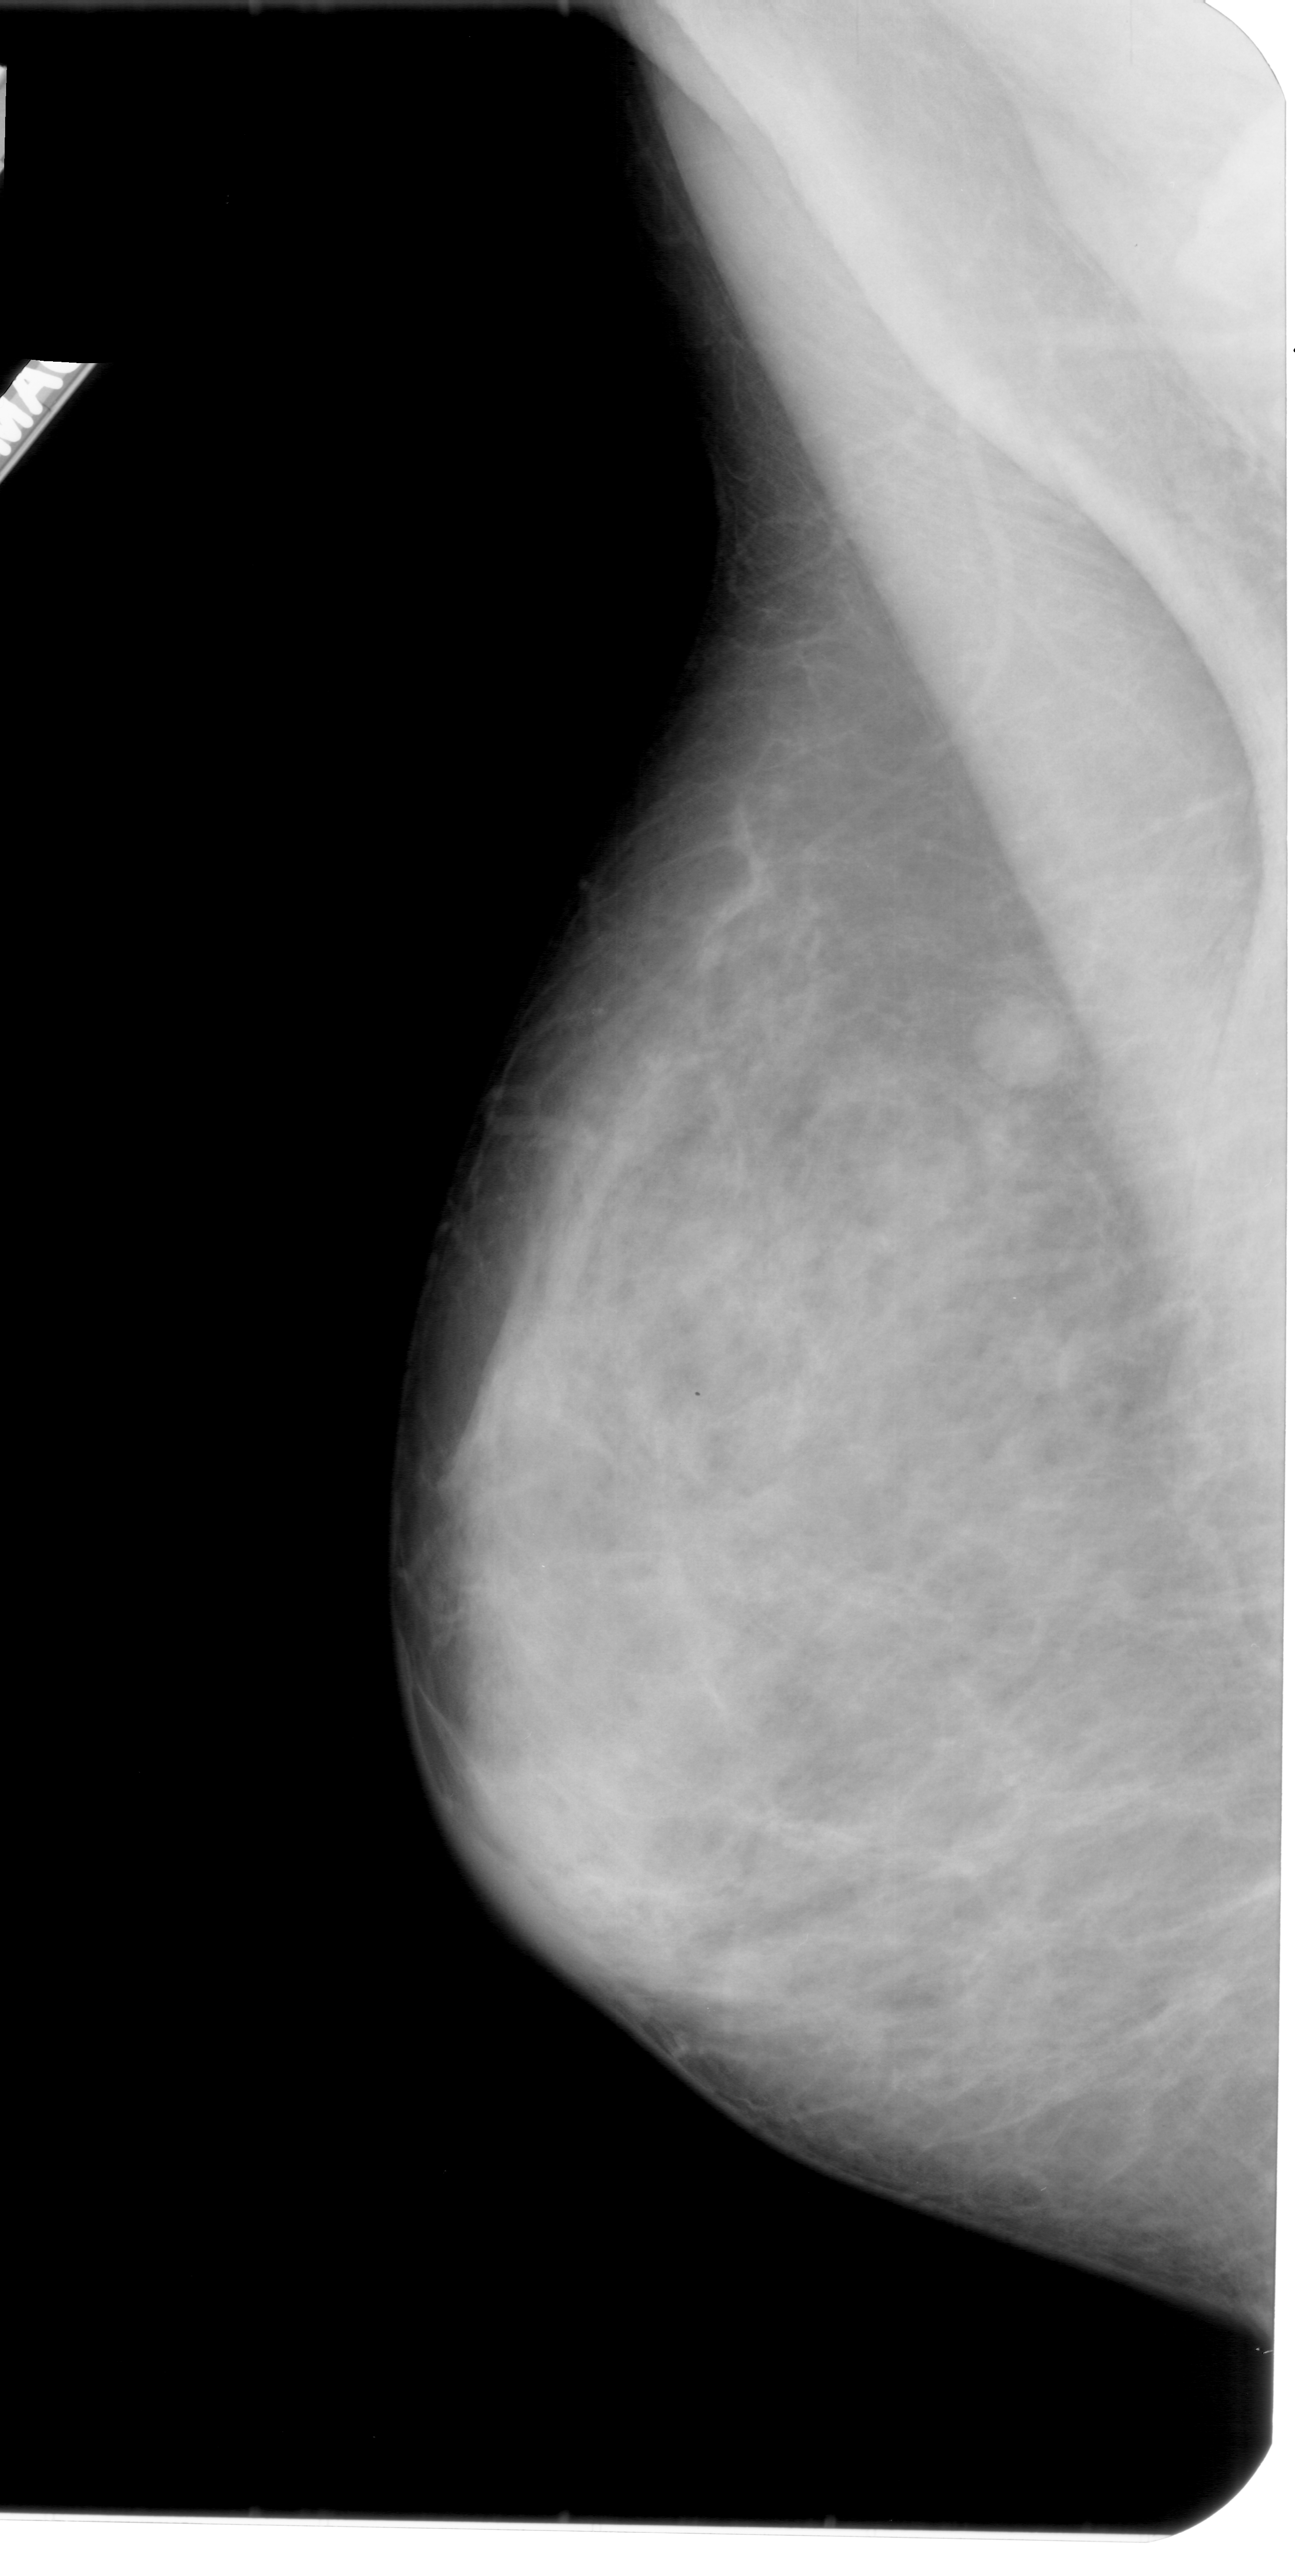
Mammogram (digitized film); left breast; mediolateral oblique (MLO) view; breast composition: heterogeneously dense (BI-RADS density category 3 of 4); 1295 × 2576 image matrix.
Marked abnormalities (boxes around the expert regions of interest):
- mass, shape round, margins circumscribed; BI-RADS assessment category 3; pathology (as recorded): benign: box from (x=971, y=993) to (x=1073, y=1093) px